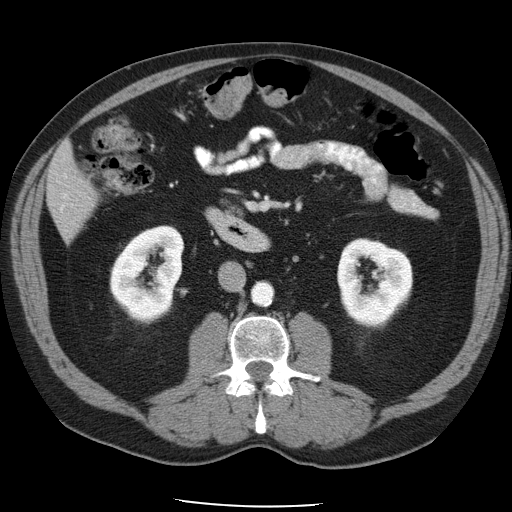
Contrast-enhanced abdominal CT, one axial slice; position 16 of 49 along the scan axis; intravenous contrast given; soft-tissue window (W 400 / L 40 HU); 5 mm slice thickness; 512 × 512 image matrix, field of view 395 × 395 mm. Male patient, age 68 years. From the clinical record (not read from this slice): diagnosis: colorectal cancer liver metastases, imaged before liver resection; multiple liver metastases: yes; largest metastasis: 1.7 cm.
Structures marked on this image (expert manual segmentation):
- liver: bounding box <48,144,97,237> (left, top, right, bottom; pixels)
- portal vein (with intrahepatic branches): <61,176,67,211>